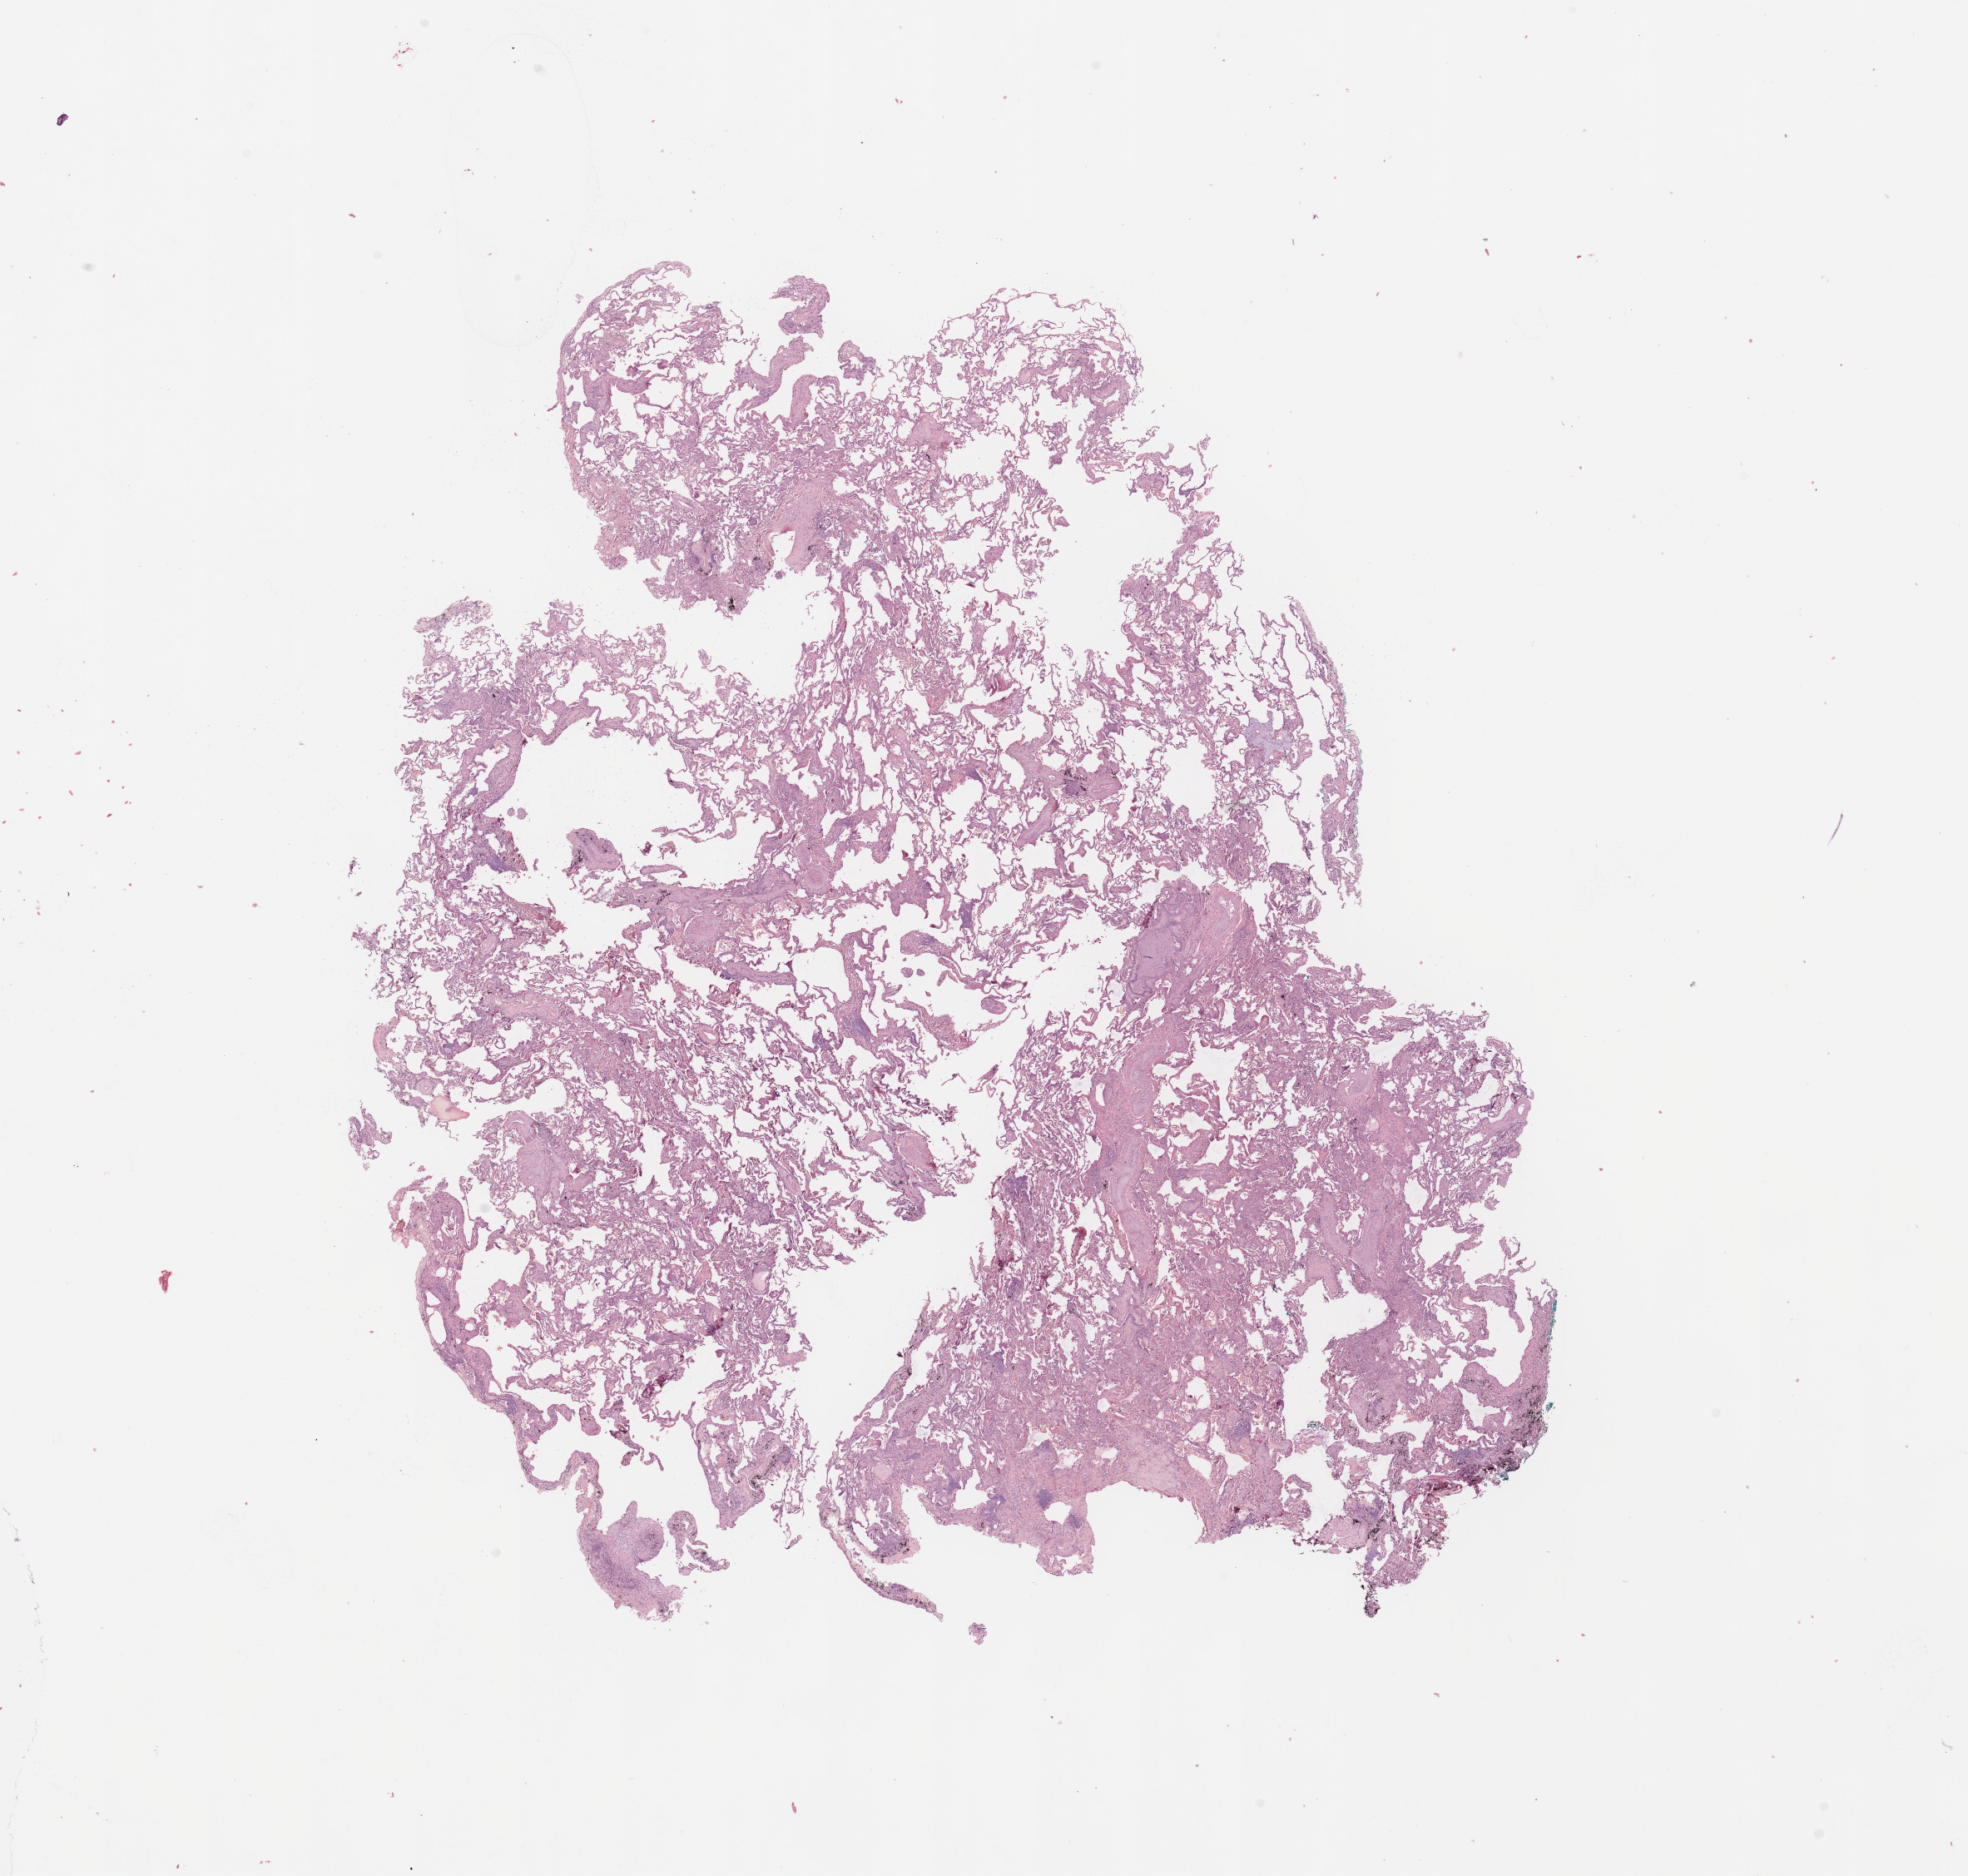
Whole-slide histology image, H&E-stained — shown as a low-resolution overview of the whole scanned area (about 18.7 x 17.8 mm). Lung, normal (non-tumour) tissue. 75-year-old male patient.
This section: normal (non-tumour) tissue from the same patient. Patient diagnosis: Squamous cell carcinoma, NOS.